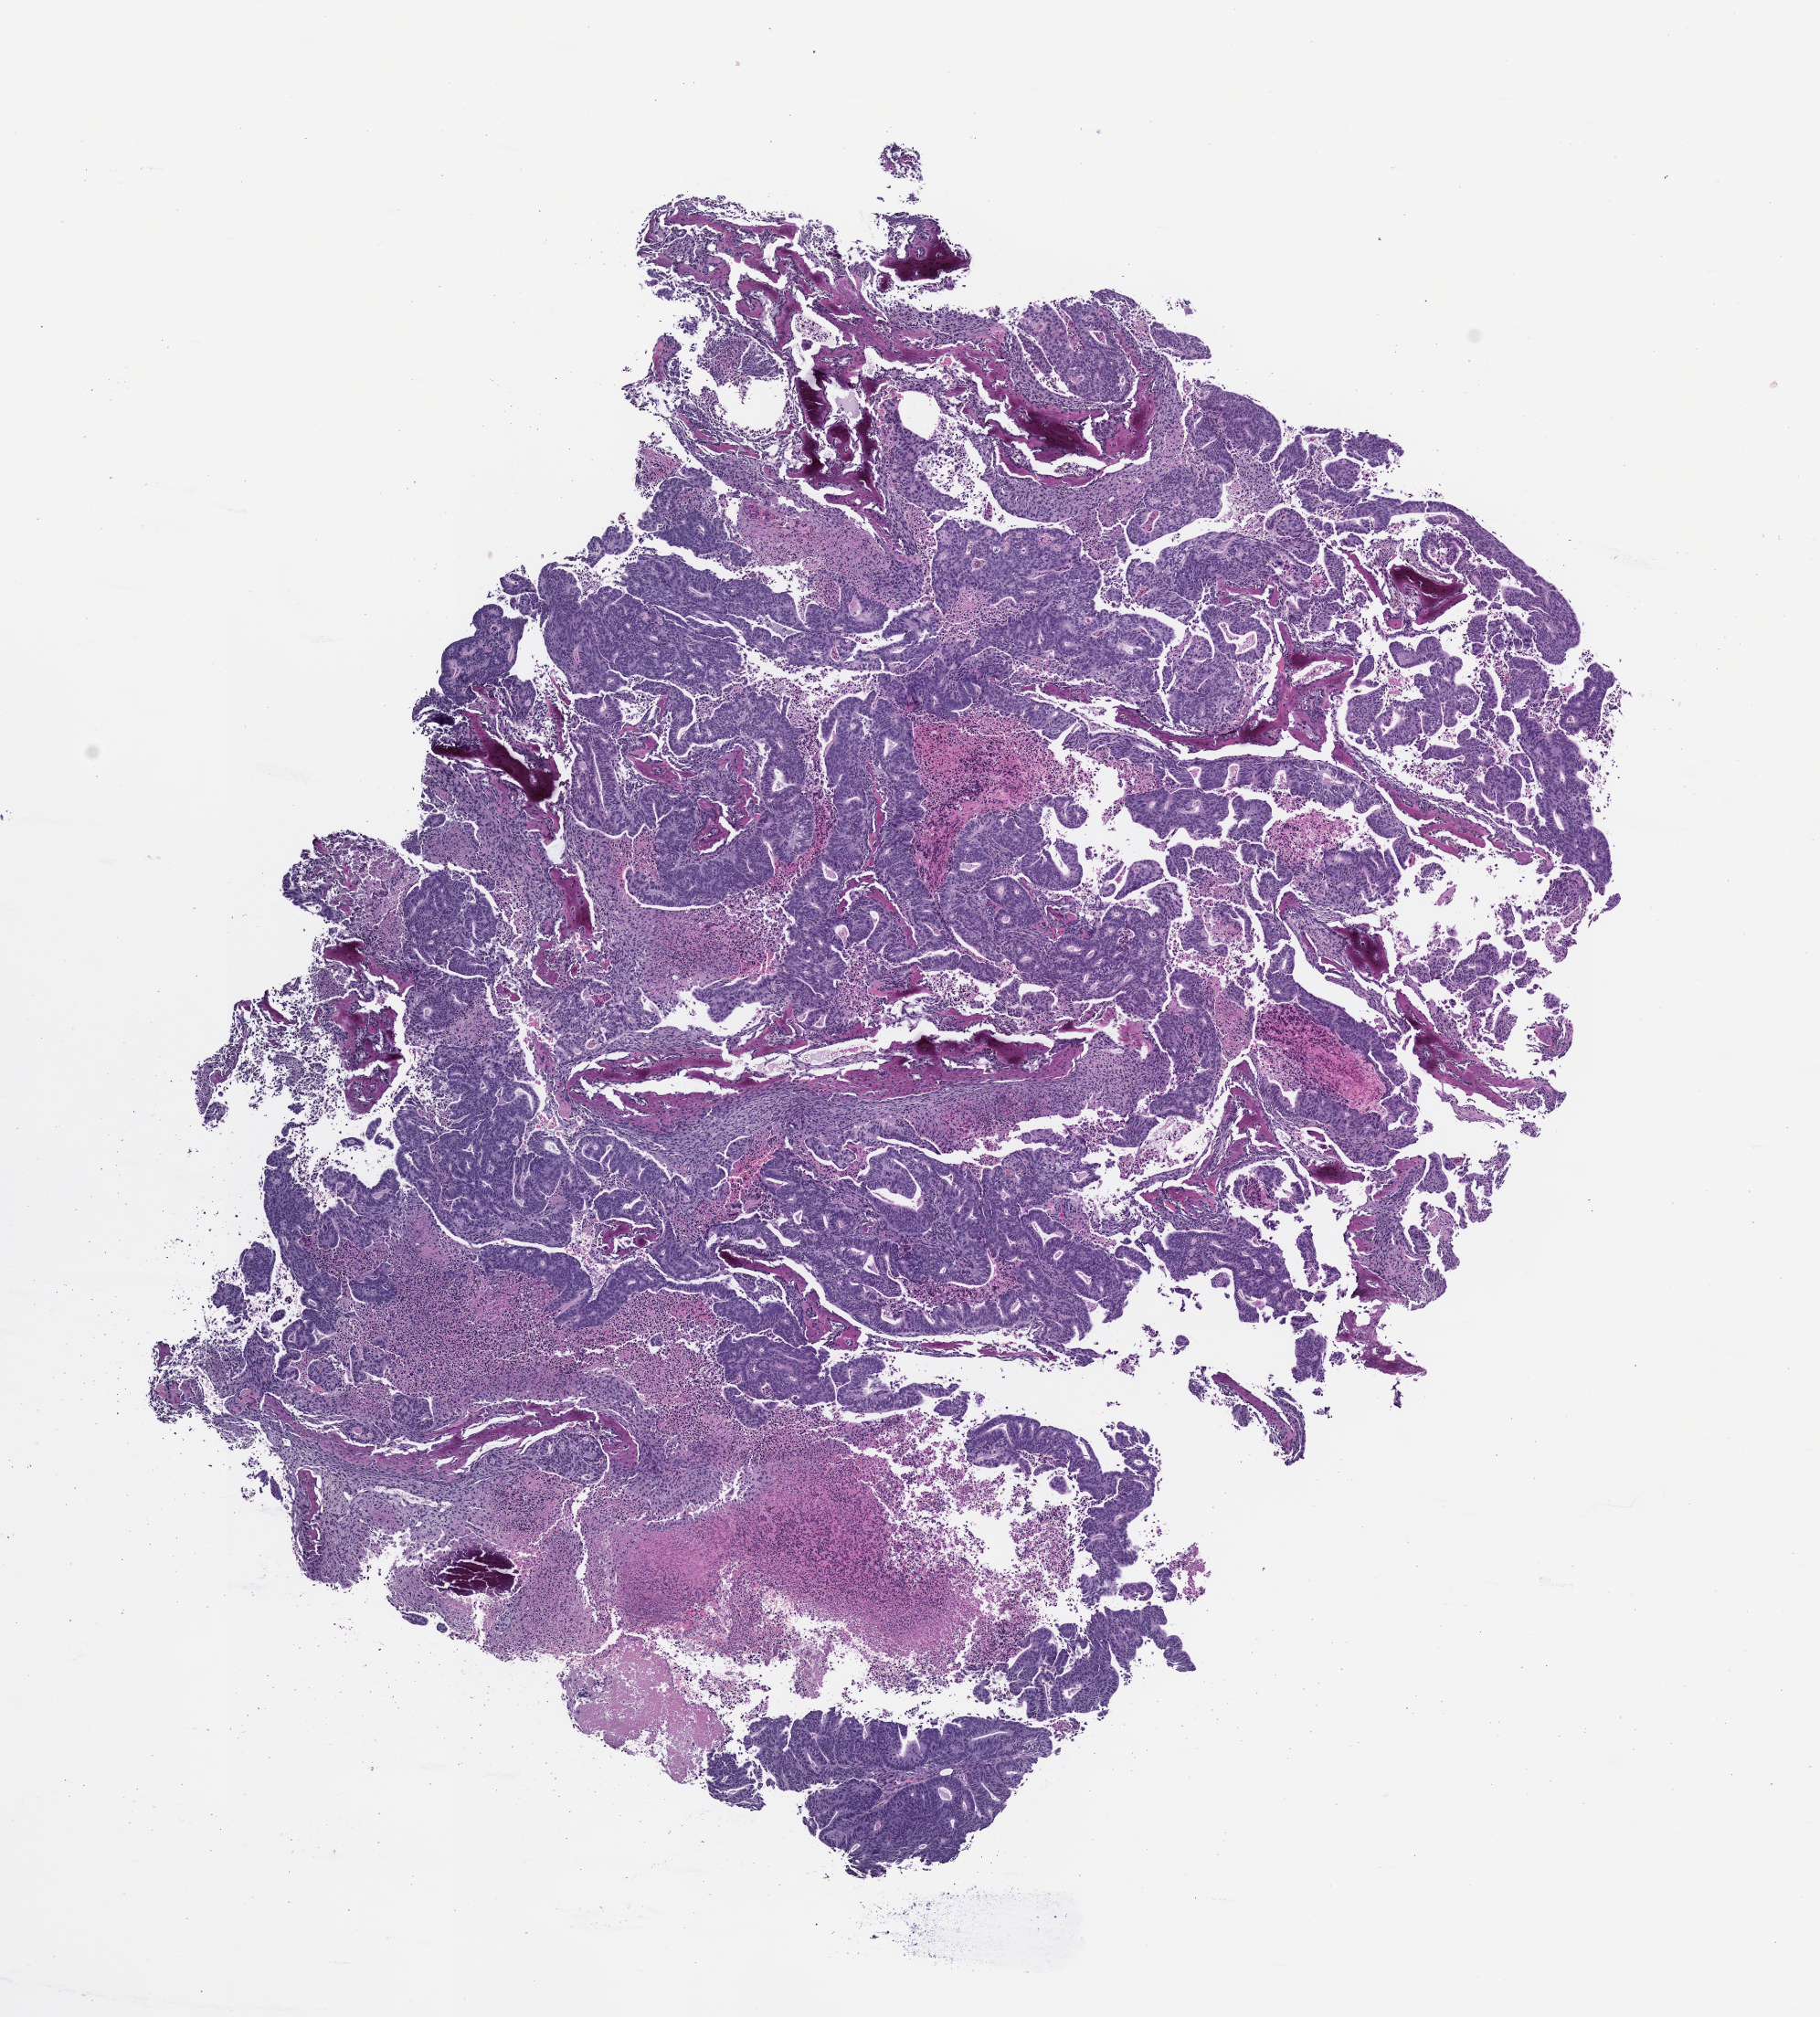
Whole-slide image, hematoxylin and eosin (H&E): patient-derived xenograft (human tumor grown in a mouse), passage 1, a low-resolution overview of the entire scanned area, about 8.0 x 8.9 mm; FFPE section; originating tumor site category: colon.
Originating patient diagnosis: Colon Adenocarcinoma.